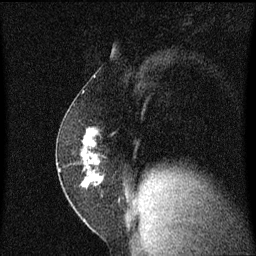
Breast MRI (dynamic contrast-enhanced), one sagittal slice; position 34 of 60 along the scan axis; dynamic contrast-enhanced series, image 2 of 3 at this slice position (ordered by acquisition); 1.5 T; TE 4.2 ms, TR 8.4 ms; 2 mm slice thickness; 256 × 256 image matrix, field of view 200 × 200 mm. Patient: female, 52 years. Case-level facts recorded for this patient, not image findings: setting: breast cancer imaged before/during neoadjuvant chemotherapy; receptor status: HER2-positive.
Structures marked on this image (semi-automatically segmented with operator editing):
- analysis volume of interest (the breast-tissue region the enhancement analysis was run in; not a lesion): bounding box <57,124,116,191> (left, top, right, bottom; pixels)
- tumour enhancement mask (voxels above the 70 % enhancement threshold inside the analysis volume of interest): <82,128,100,187>